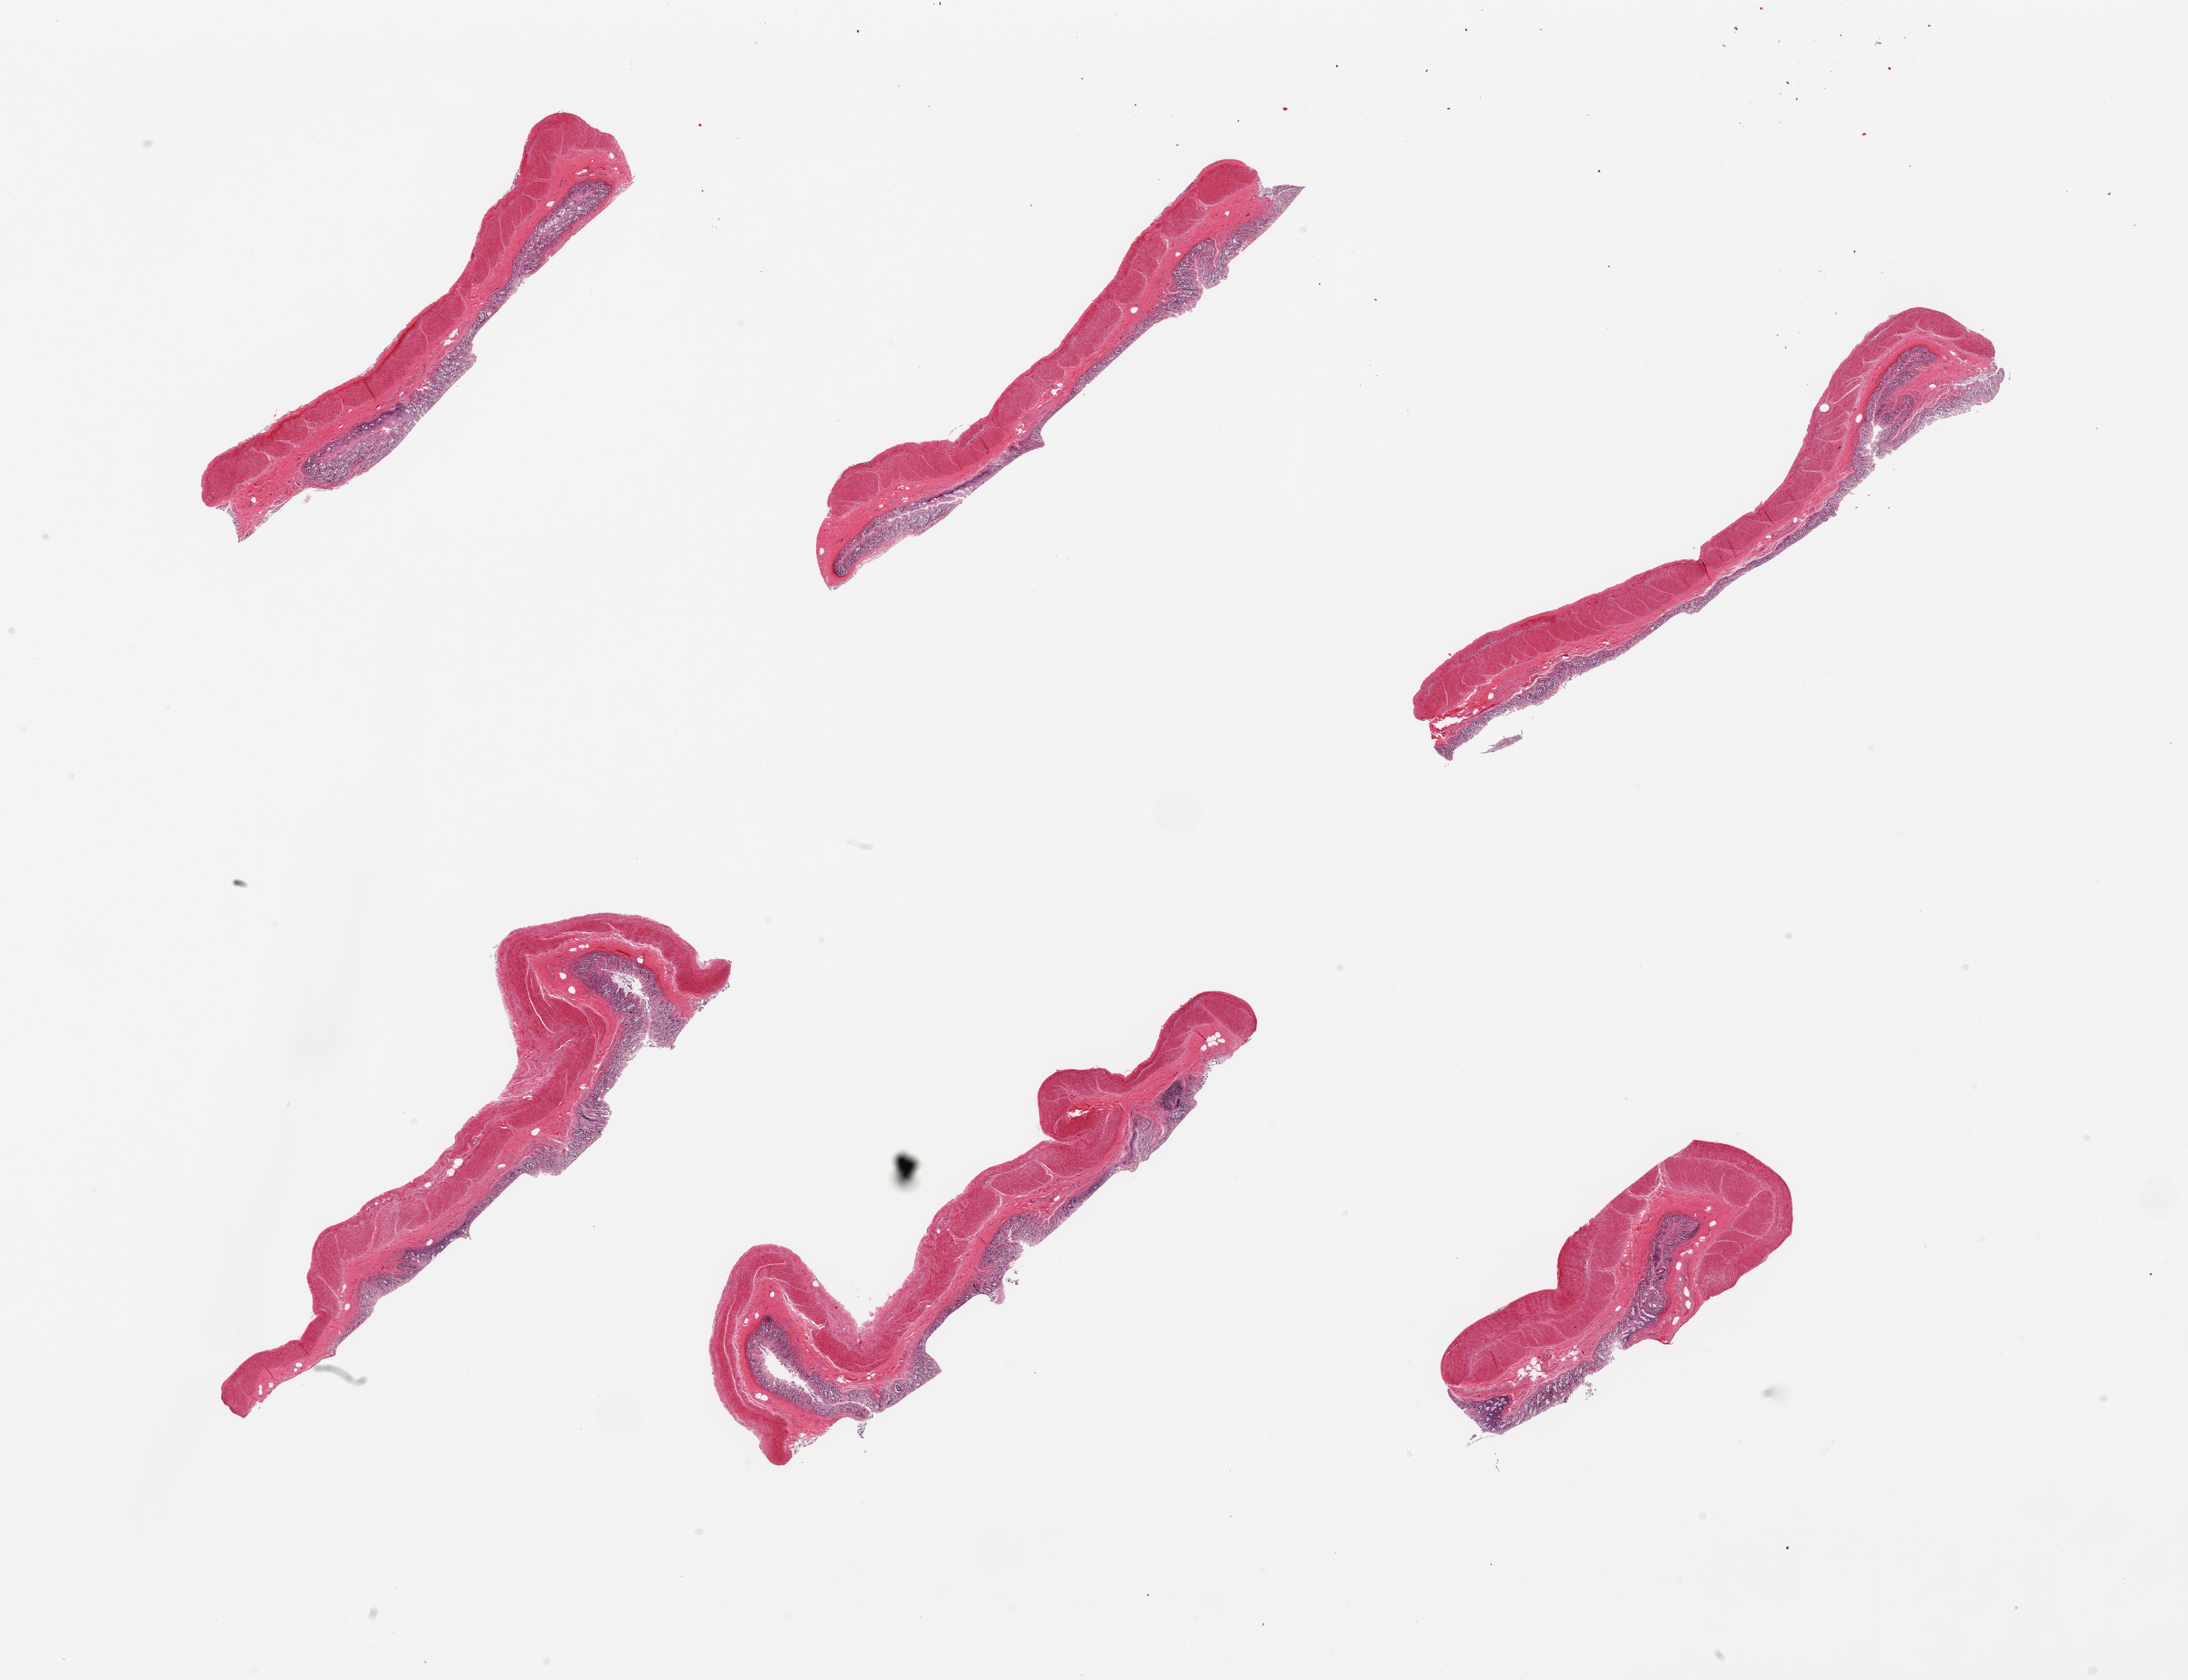
Whole-slide image, H&E stain, brightfield — low-resolution overview of the scanned area, about 27.6 x 21.2 mm. PAXgene-fixed, paraffin-embedded tissue. Section of transverse colon (target tissue). Donor tissue sample. Donor: male.
Reviewer comment on this tissue sample: 6 pieces, mucosa is ~0.3mm, advanced autolysis.